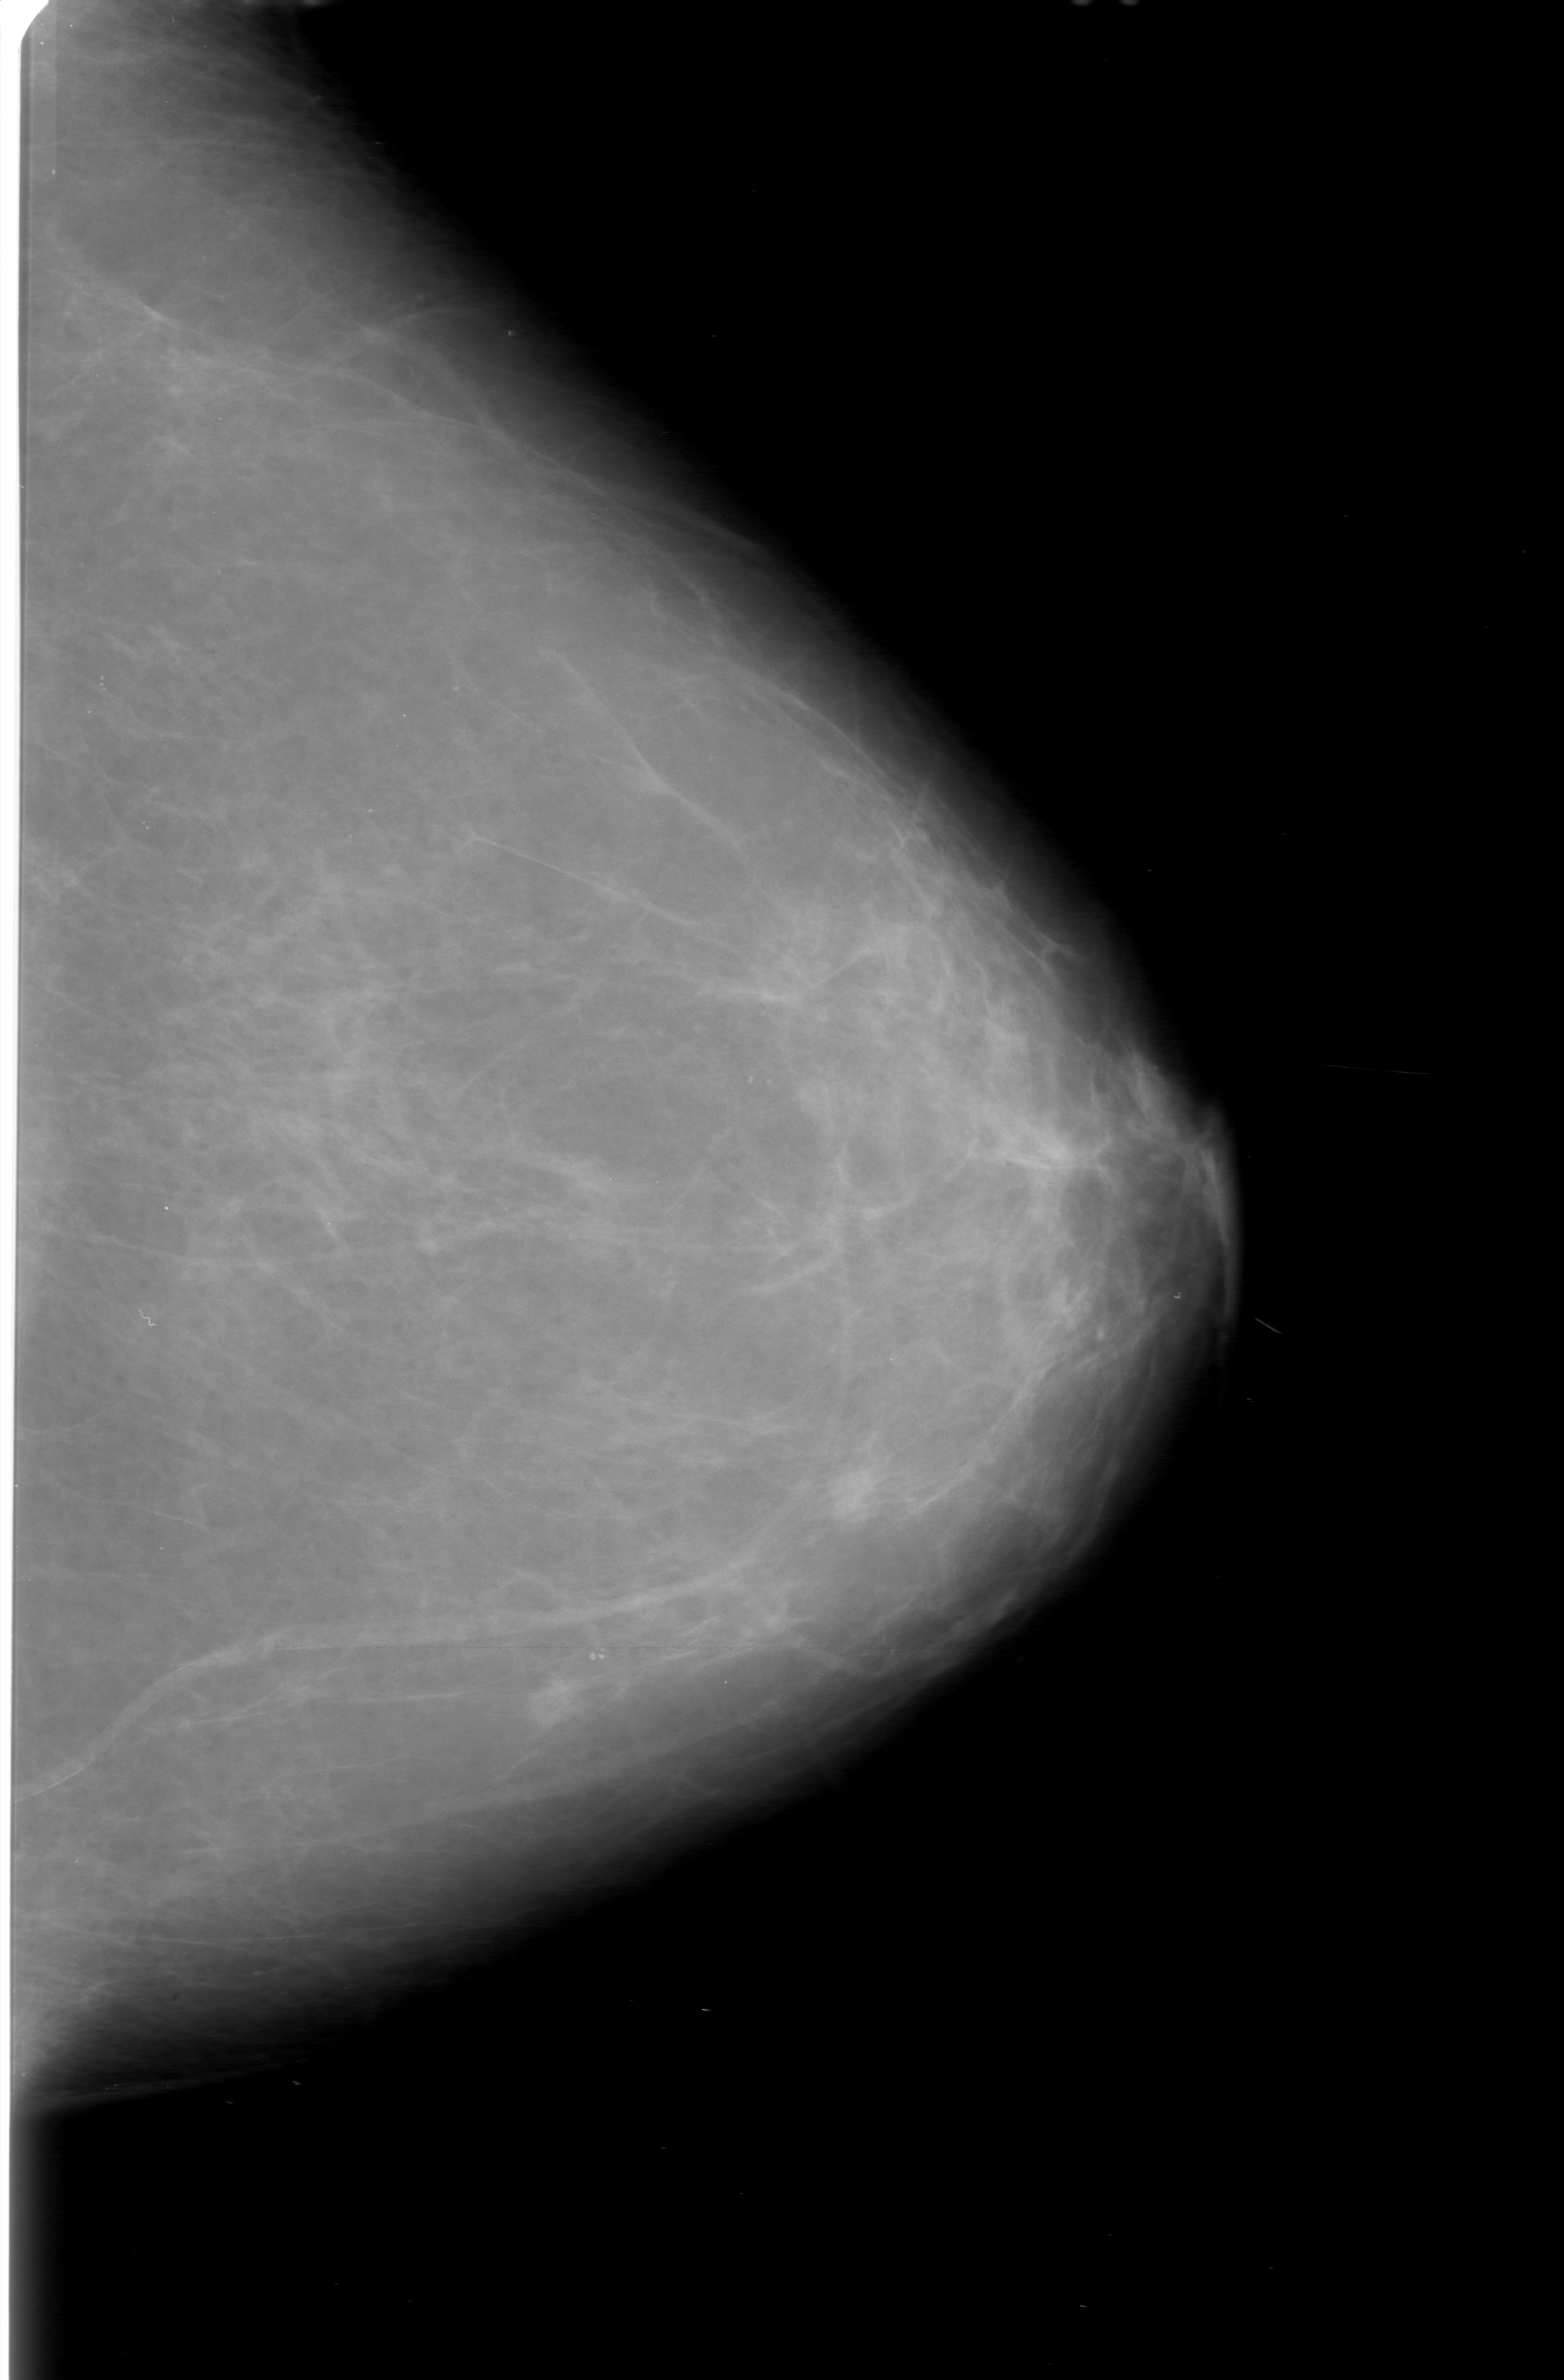
Scanned film-screen mammogram. Left breast. Craniocaudal (CC) view. Breast composition: almost entirely fatty (BI-RADS density category 1 of 4). 1564 × 2380 image matrix.
Expert-marked regions of interest on this film, with their recorded descriptors:
- mass, shape lobulated, margins obscured; BI-RADS assessment category 0 (incomplete: needs additional imaging); subtlety rating 4 on a 1 (subtle) to 5 (obvious) scale; pathology (as recorded): malignant: bounding box (x1, y1, x2, y2) in pixels: (512, 1659, 592, 1746)